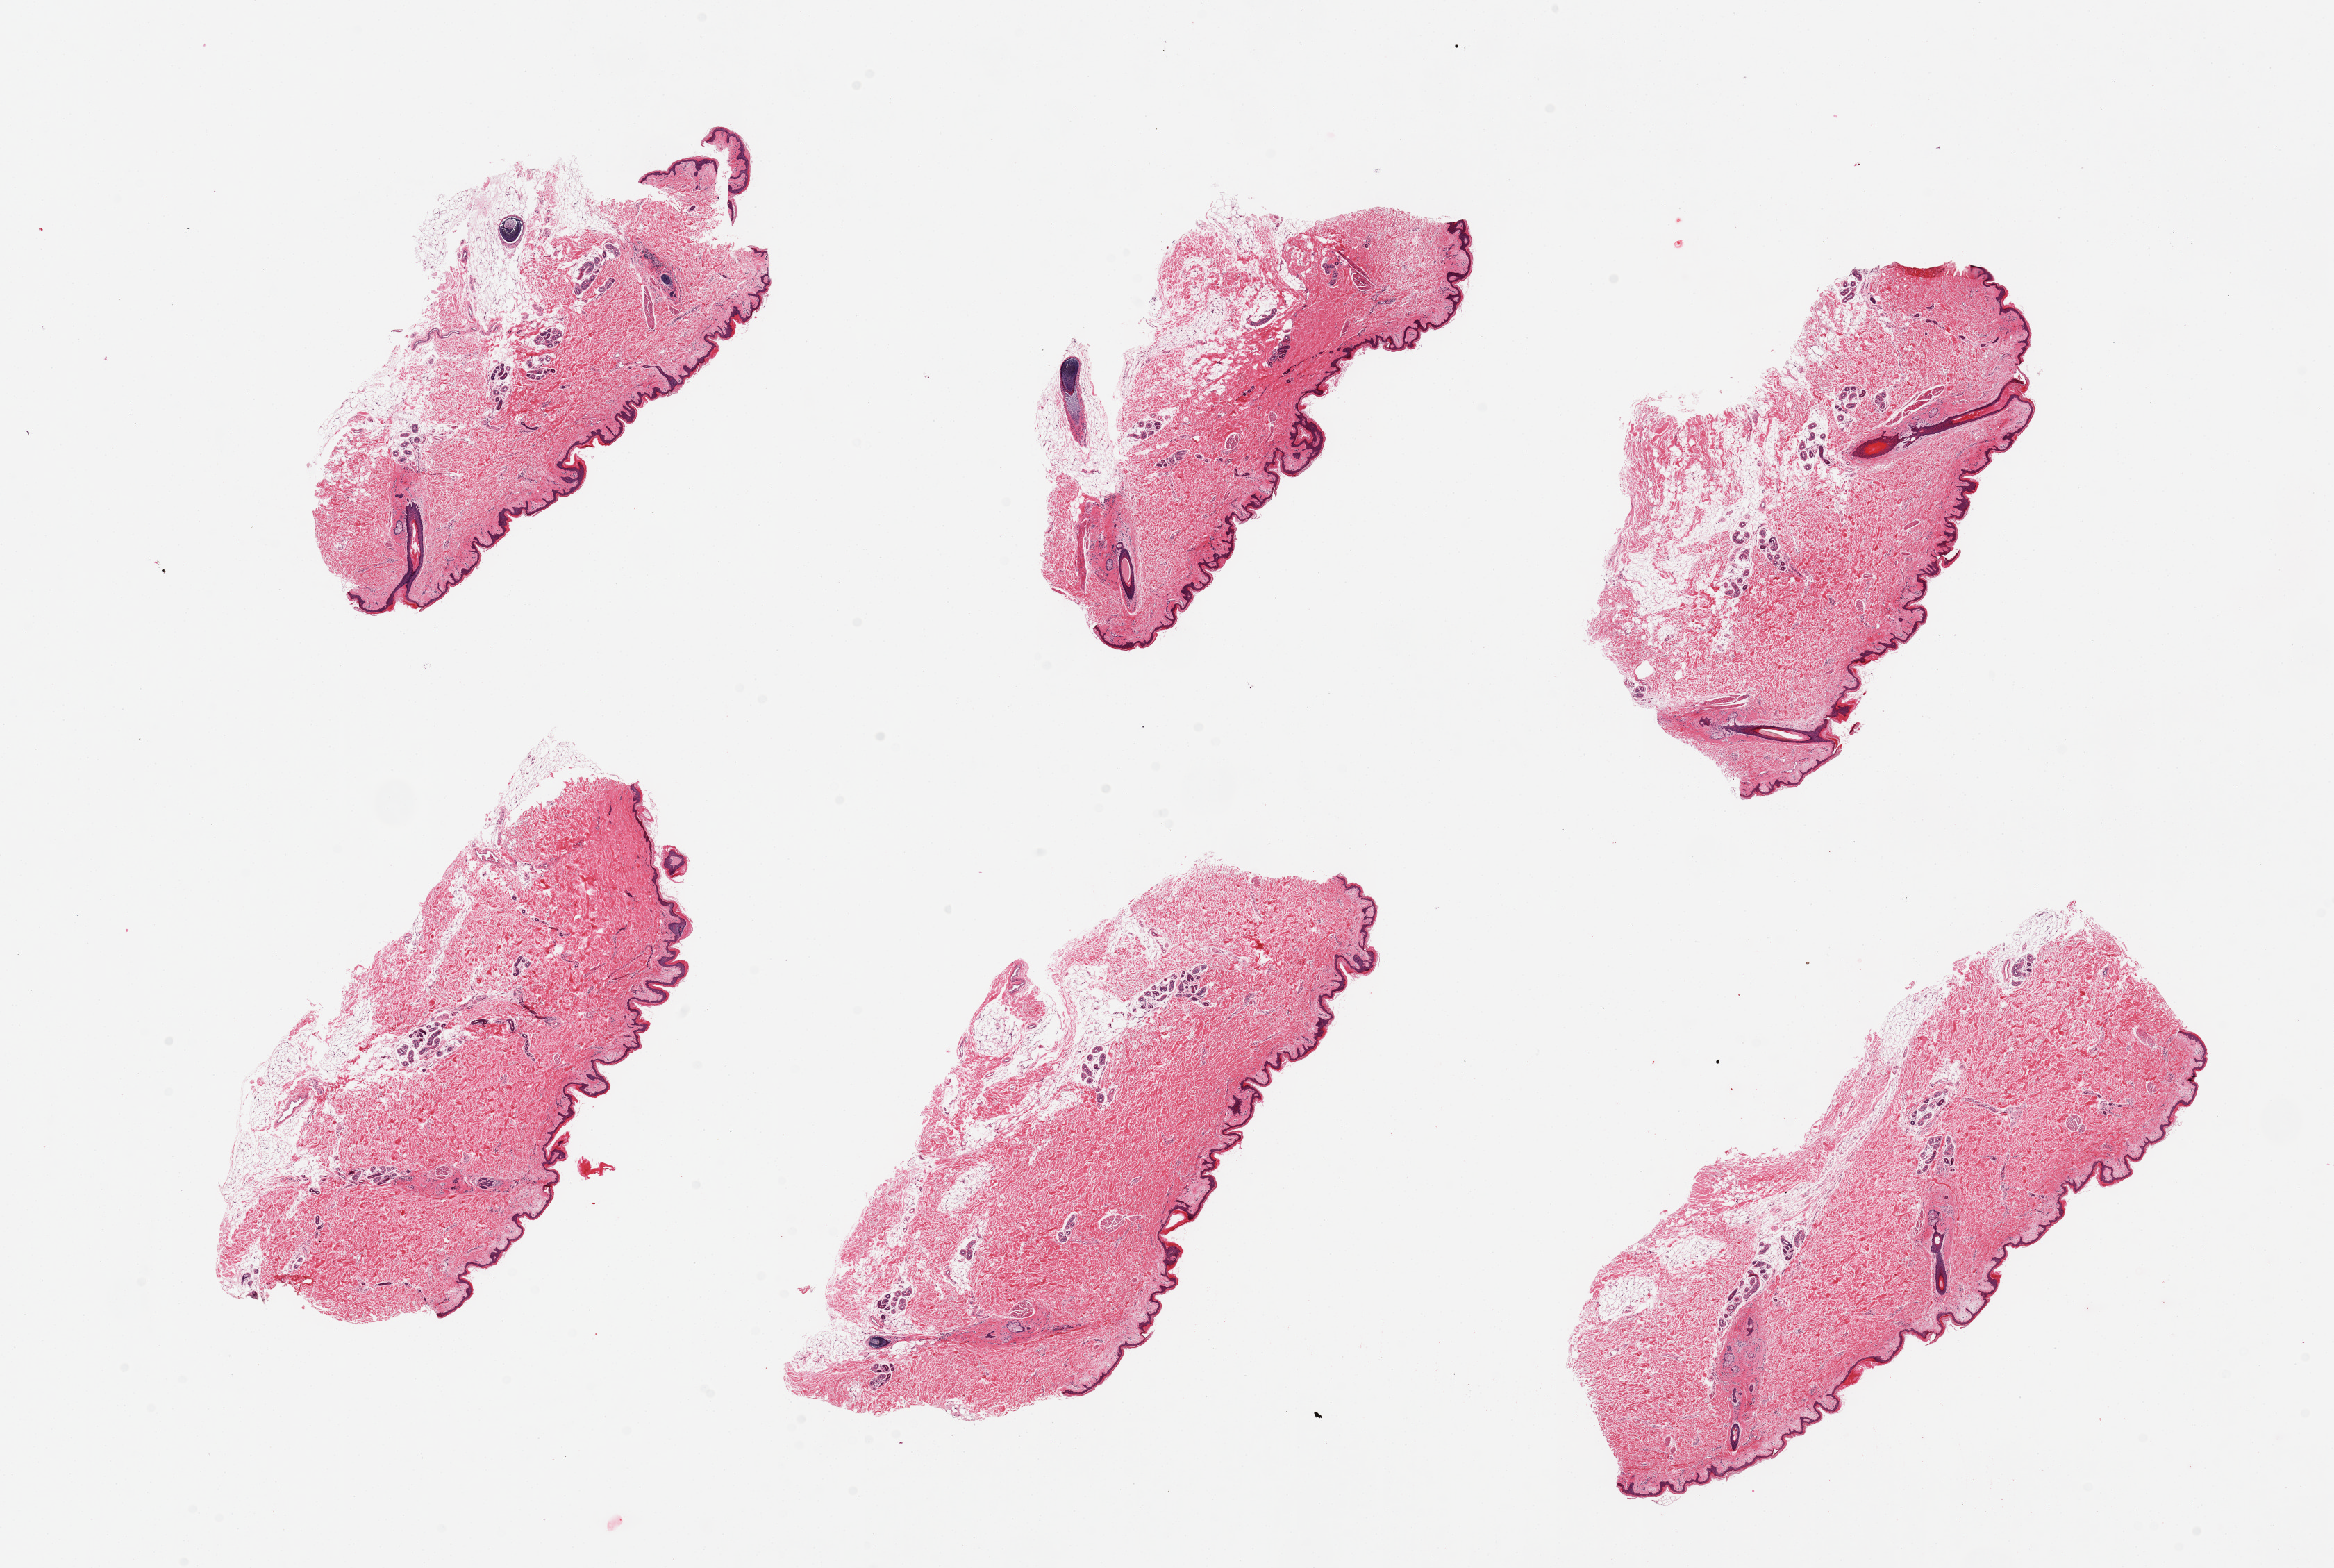
Digitized H&E-stained section — a low-resolution overview of the entire scanned area, about 26.6 x 17.9 mm; PAXgene-fixed paraffin-embedded (PFPE) section; section of skin of suprapubic region (target tissue); tissue donor sample. Donor: male.
- reviewer comment on this tissue sample: 6 pieces. Well trimmed